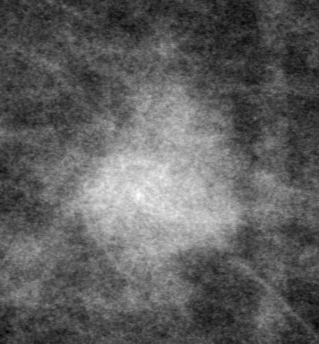
Crop from a digitized film mammogram around one marked abnormality; left breast; CC view.
Mass, shape oval, margins obscured; BI-RADS assessment category 0 (incomplete: needs additional imaging); subtlety rating 4 on a 1 (subtle) to 5 (obvious) scale; pathology (as recorded): benign.